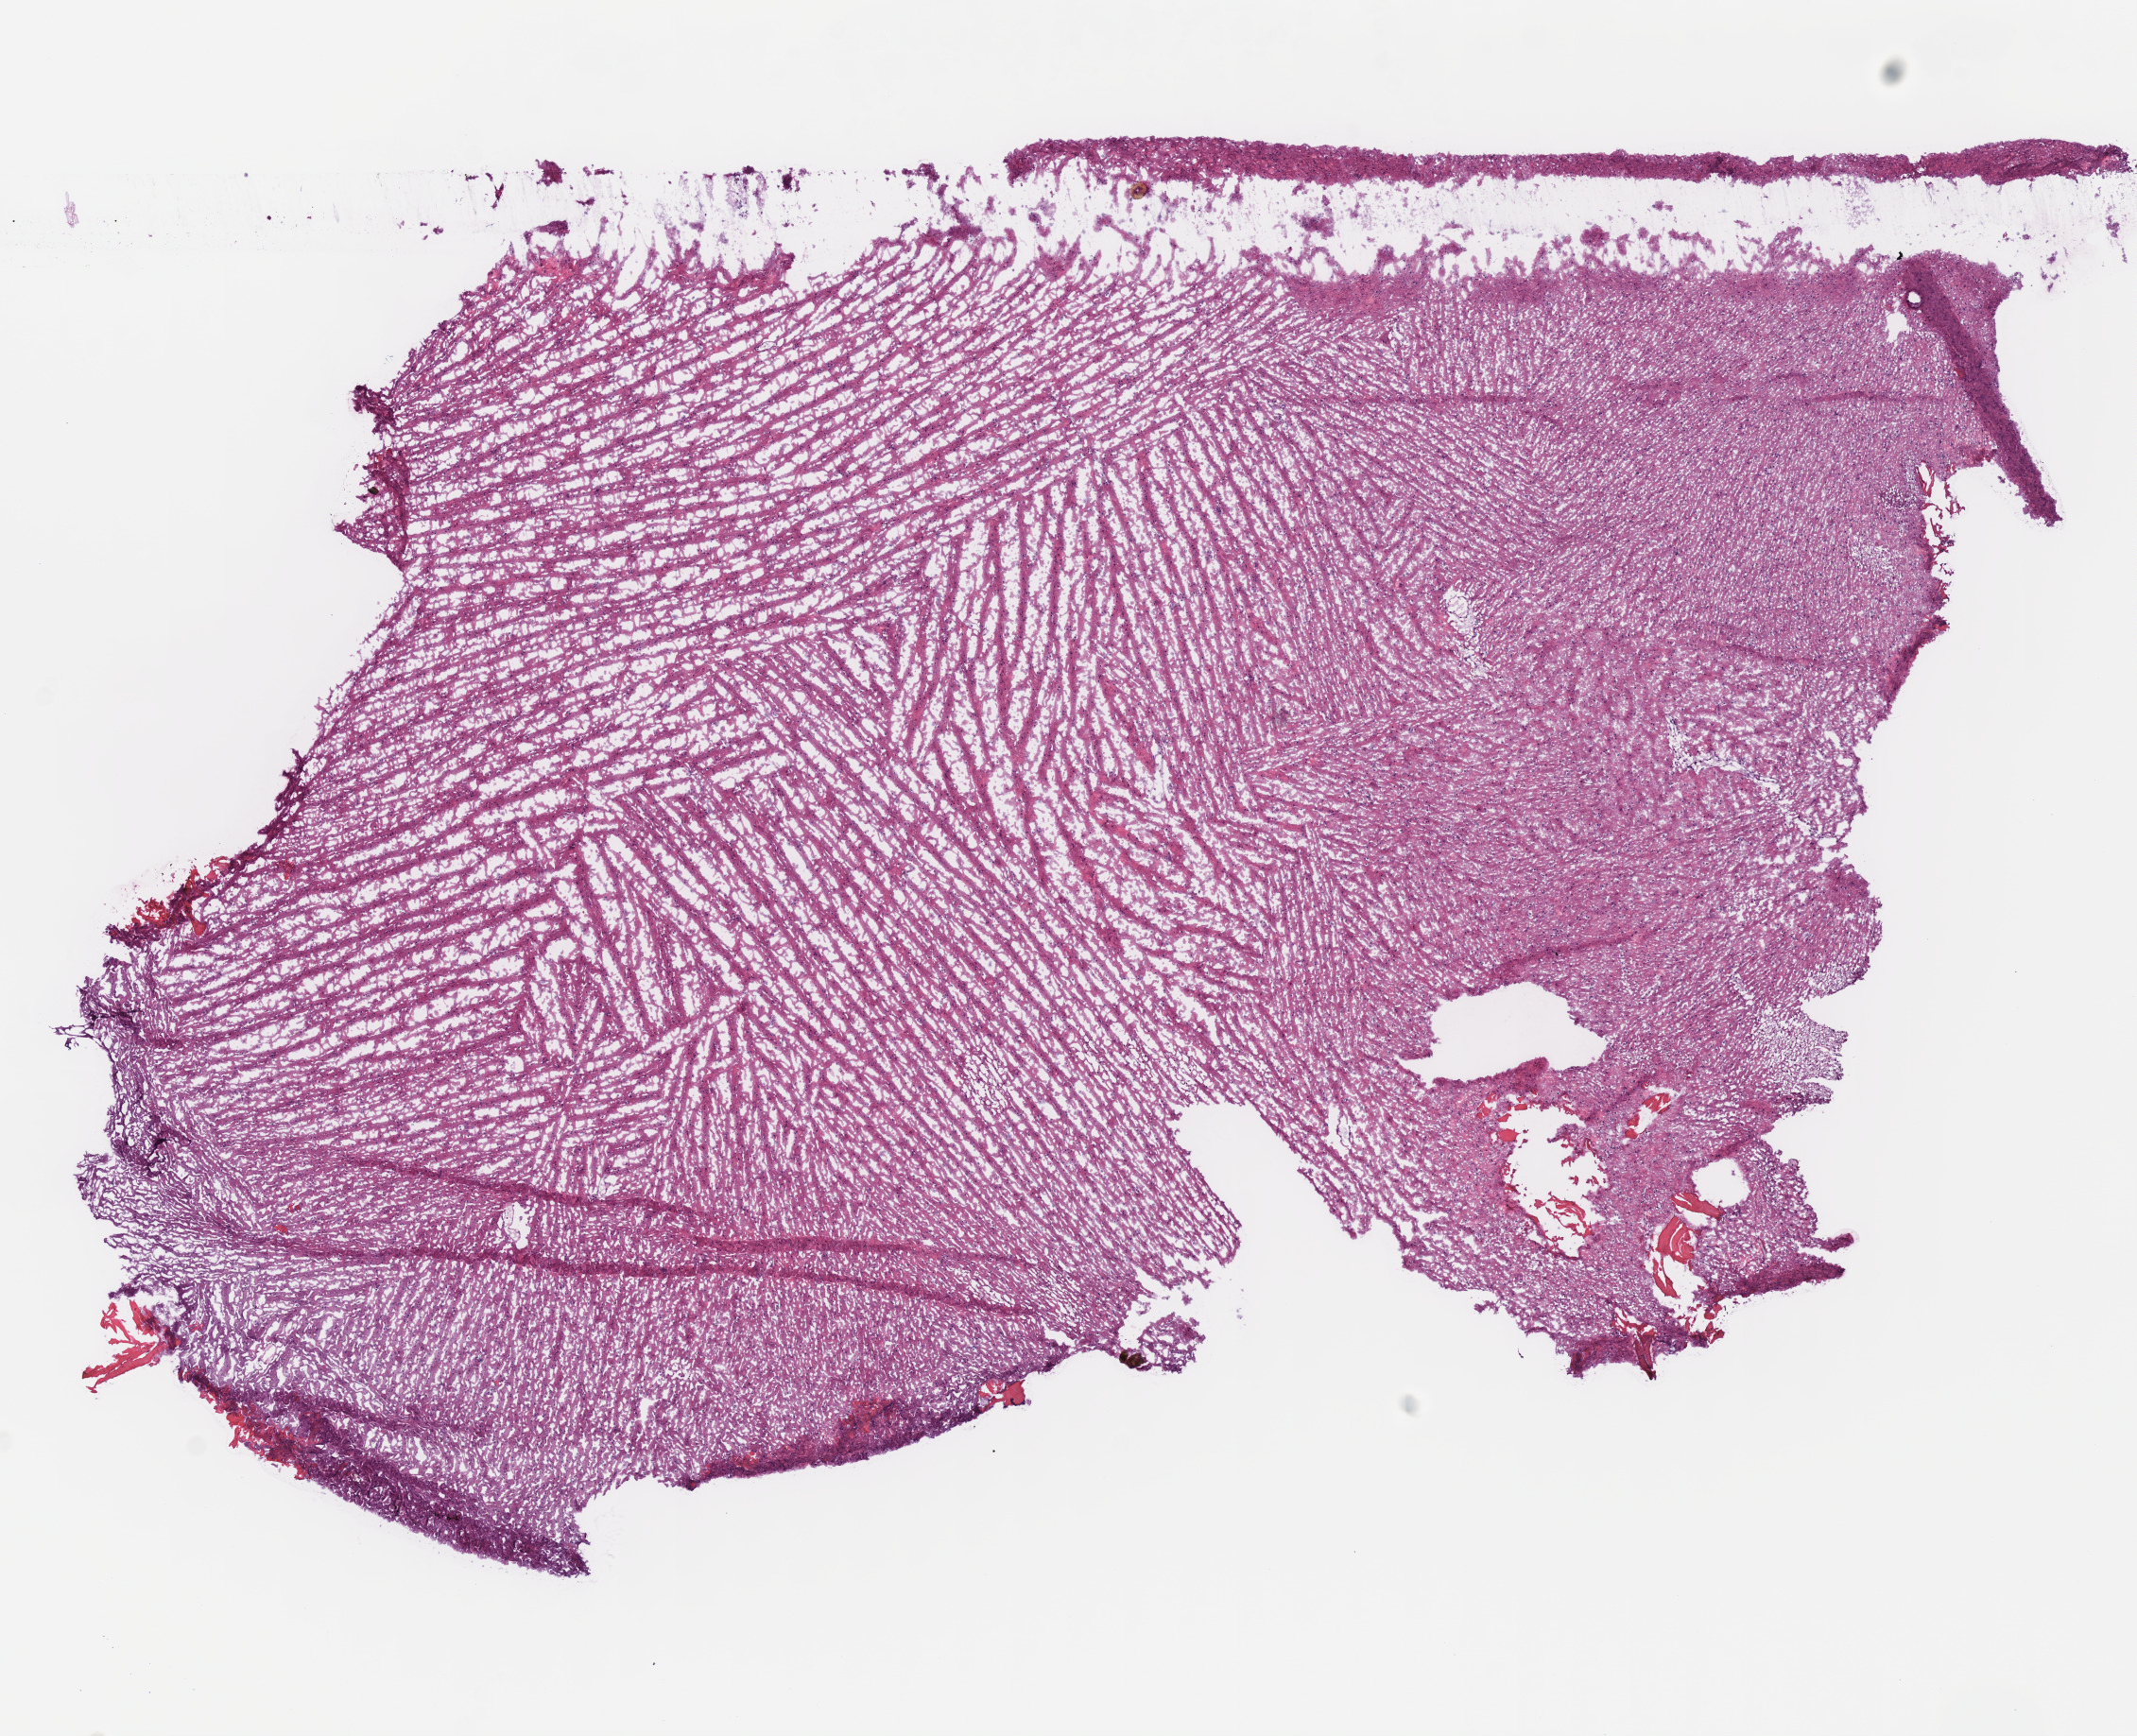
Whole-slide histology image, H&E, whole scanned area (about 8.9 x 7.2 mm) shown as a low-resolution overview, frozen section from the bottom of the tissue portion, sample: primary tumour, brain. Male patient; age at initial diagnosis 37 years. Histologic grade: G2 (moderately differentiated).
Pathologic diagnosis: Oligodendroglioma, NOS.